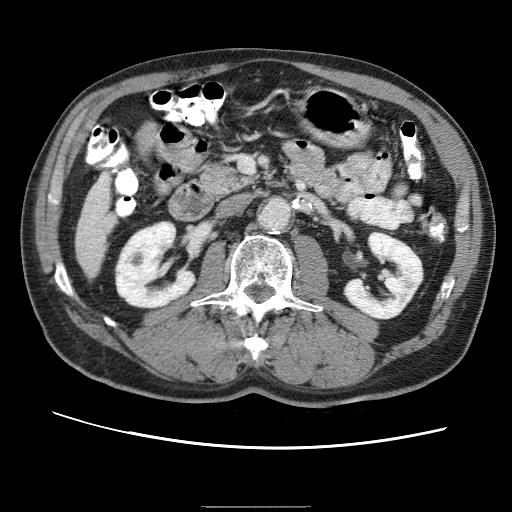
Contrast-enhanced abdominal CT (liver protocol), one axial slice; slice 7 of 75 in the series (ordered by position); reconstruction kernel STANDARD; one of 2 acquisitions stored at this slice position; soft-tissue window (W 400 / L 40 HU); 2.5 mm slice thickness; 512 × 512 image matrix, field of view 360 × 360 mm. From the clinical record (not read from this slice): diagnosis: hepatocellular carcinoma (patient treated with transarterial chemoembolisation; whether this scan precedes or follows treatment is not stated here); TNM stage (as recorded): Stage-II; Child-Pugh class: A; tumour differentiation: well differentiated.
Structures marked on this image (semi-automatic segmentation, software-assisted and operator-edited):
- liver parenchyma outside the tumour (the mass and vessels are separate outlines, so this box may not span the whole liver): box from (x=76, y=184) to (x=102, y=262) px
- liver vessels: (x=83, y=187)–(x=101, y=224)